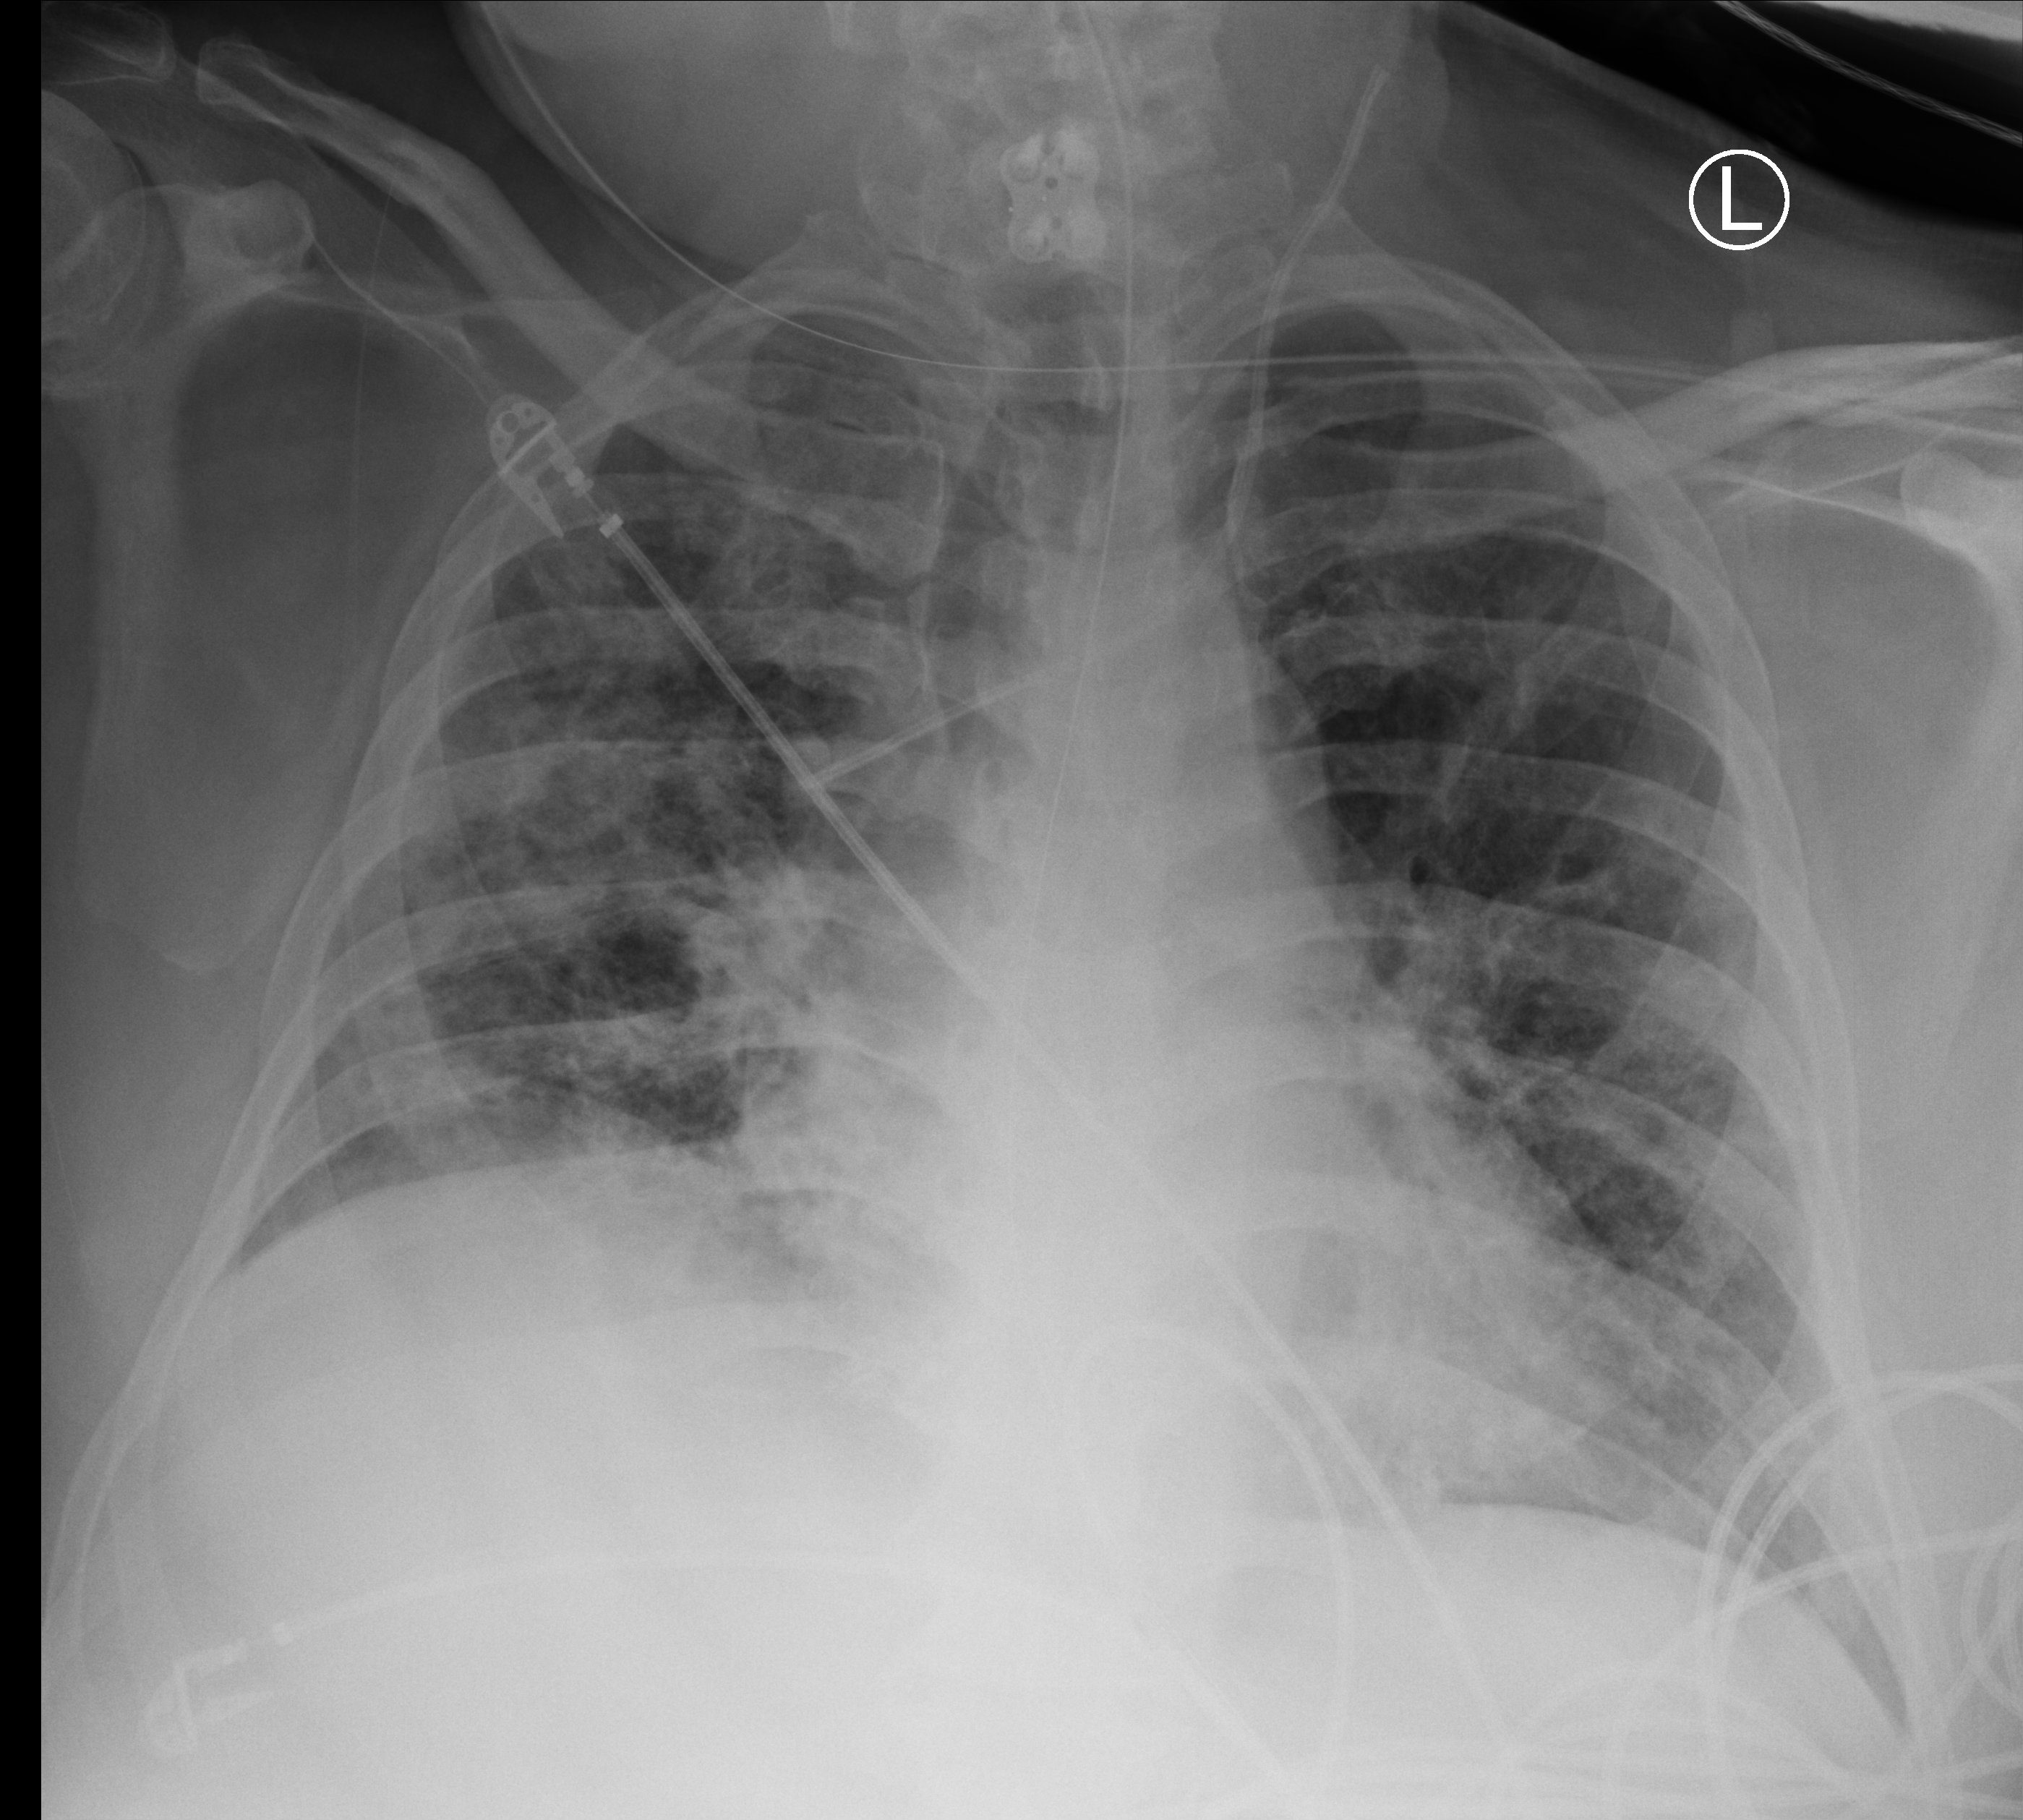
Chest X-ray (portable). Male patient hospitalised with COVID-19, age 18–59 years.
Admission-level facts for this patient (not findings on this image; timing relative to this image not recorded): admitted to intensive care during this hospital stay: yes; smoking status (admission record): never; mechanically ventilated during this hospital stay: yes.